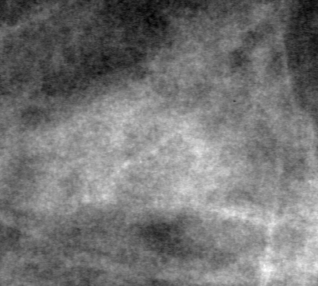
Cropped region of a digitized screen-film mammogram centred on a radiologist-marked abnormality; right breast; CC view.
Marked abnormality: mass, shape oval, margins obscured; BI-RADS assessment category 4; pathology (as recorded): benign.